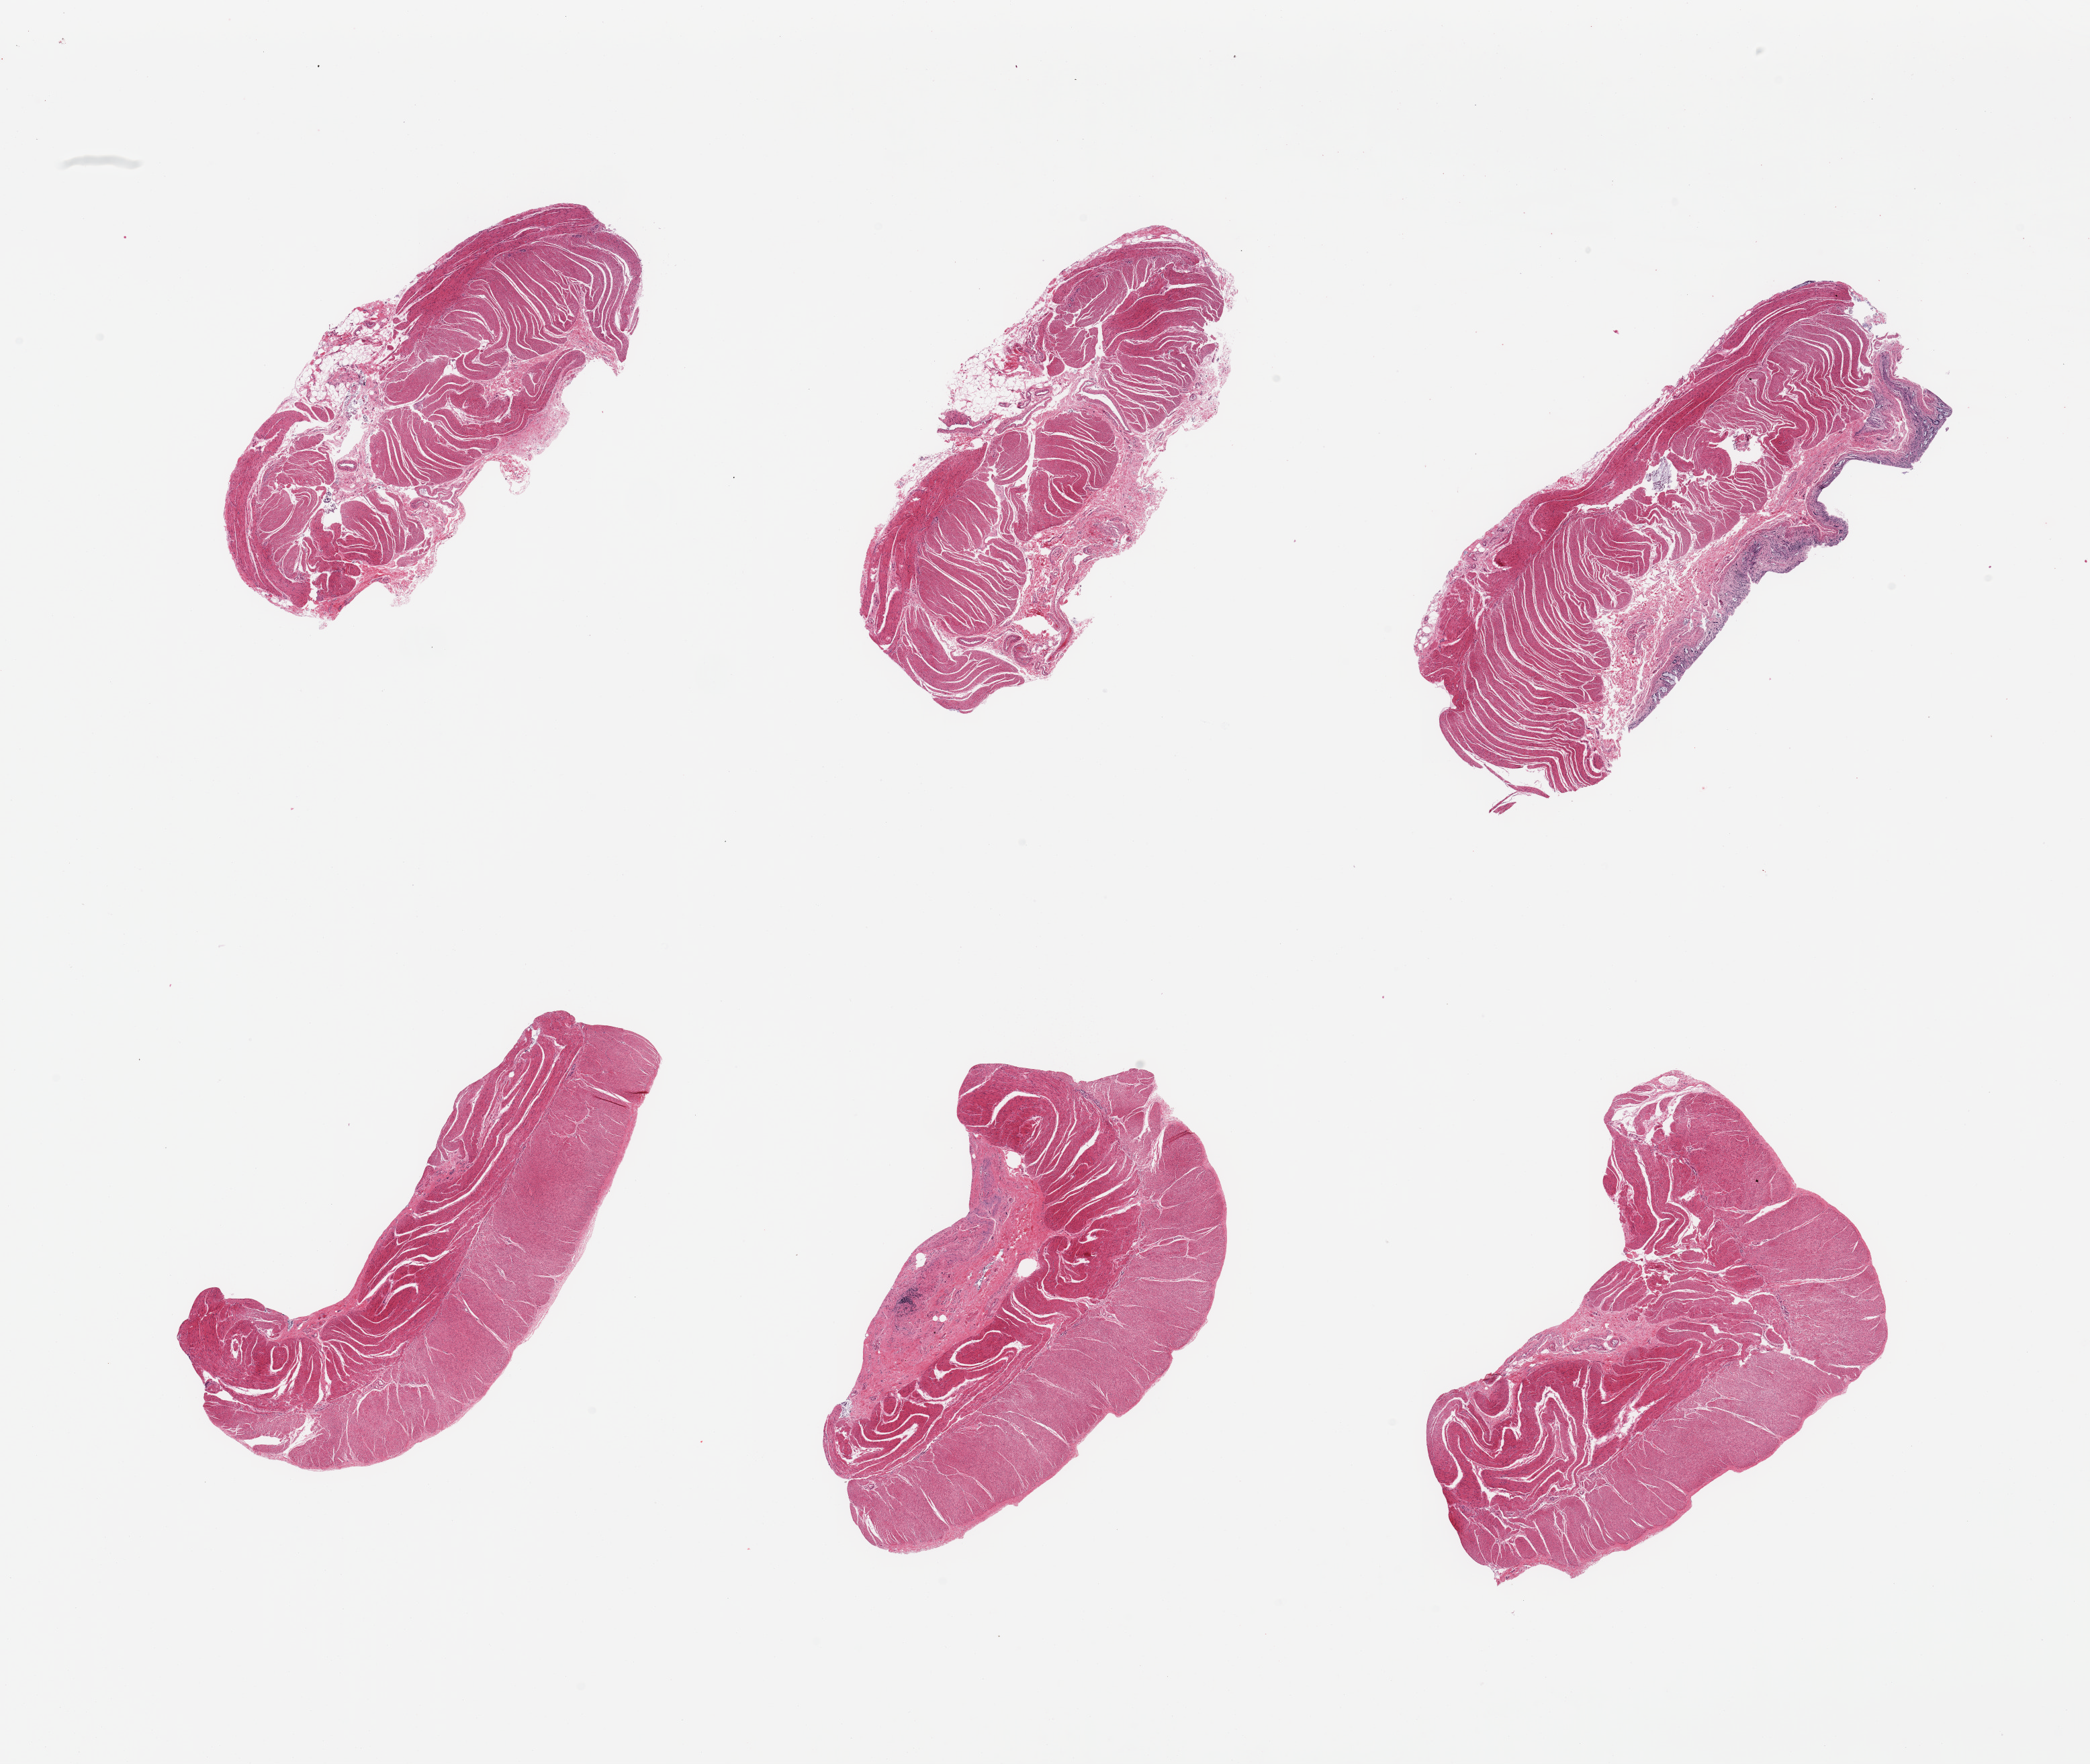
Whole-slide image, haematoxylin and eosin stain — low-resolution overview of the scanned area, about 24.6 x 20.8 mm (acquisition: 20x scan), PAXgene-fixed, paraffin-embedded tissue, section of sigmoid colon (target tissue), tissue donor sample. Donor sex: male.
Reviewer comment on this tissue sample: 6 pieces; portion of autolyzed mucosa in 1 piece; variable amounts of submucosa in 5 pieces up to 25% area.